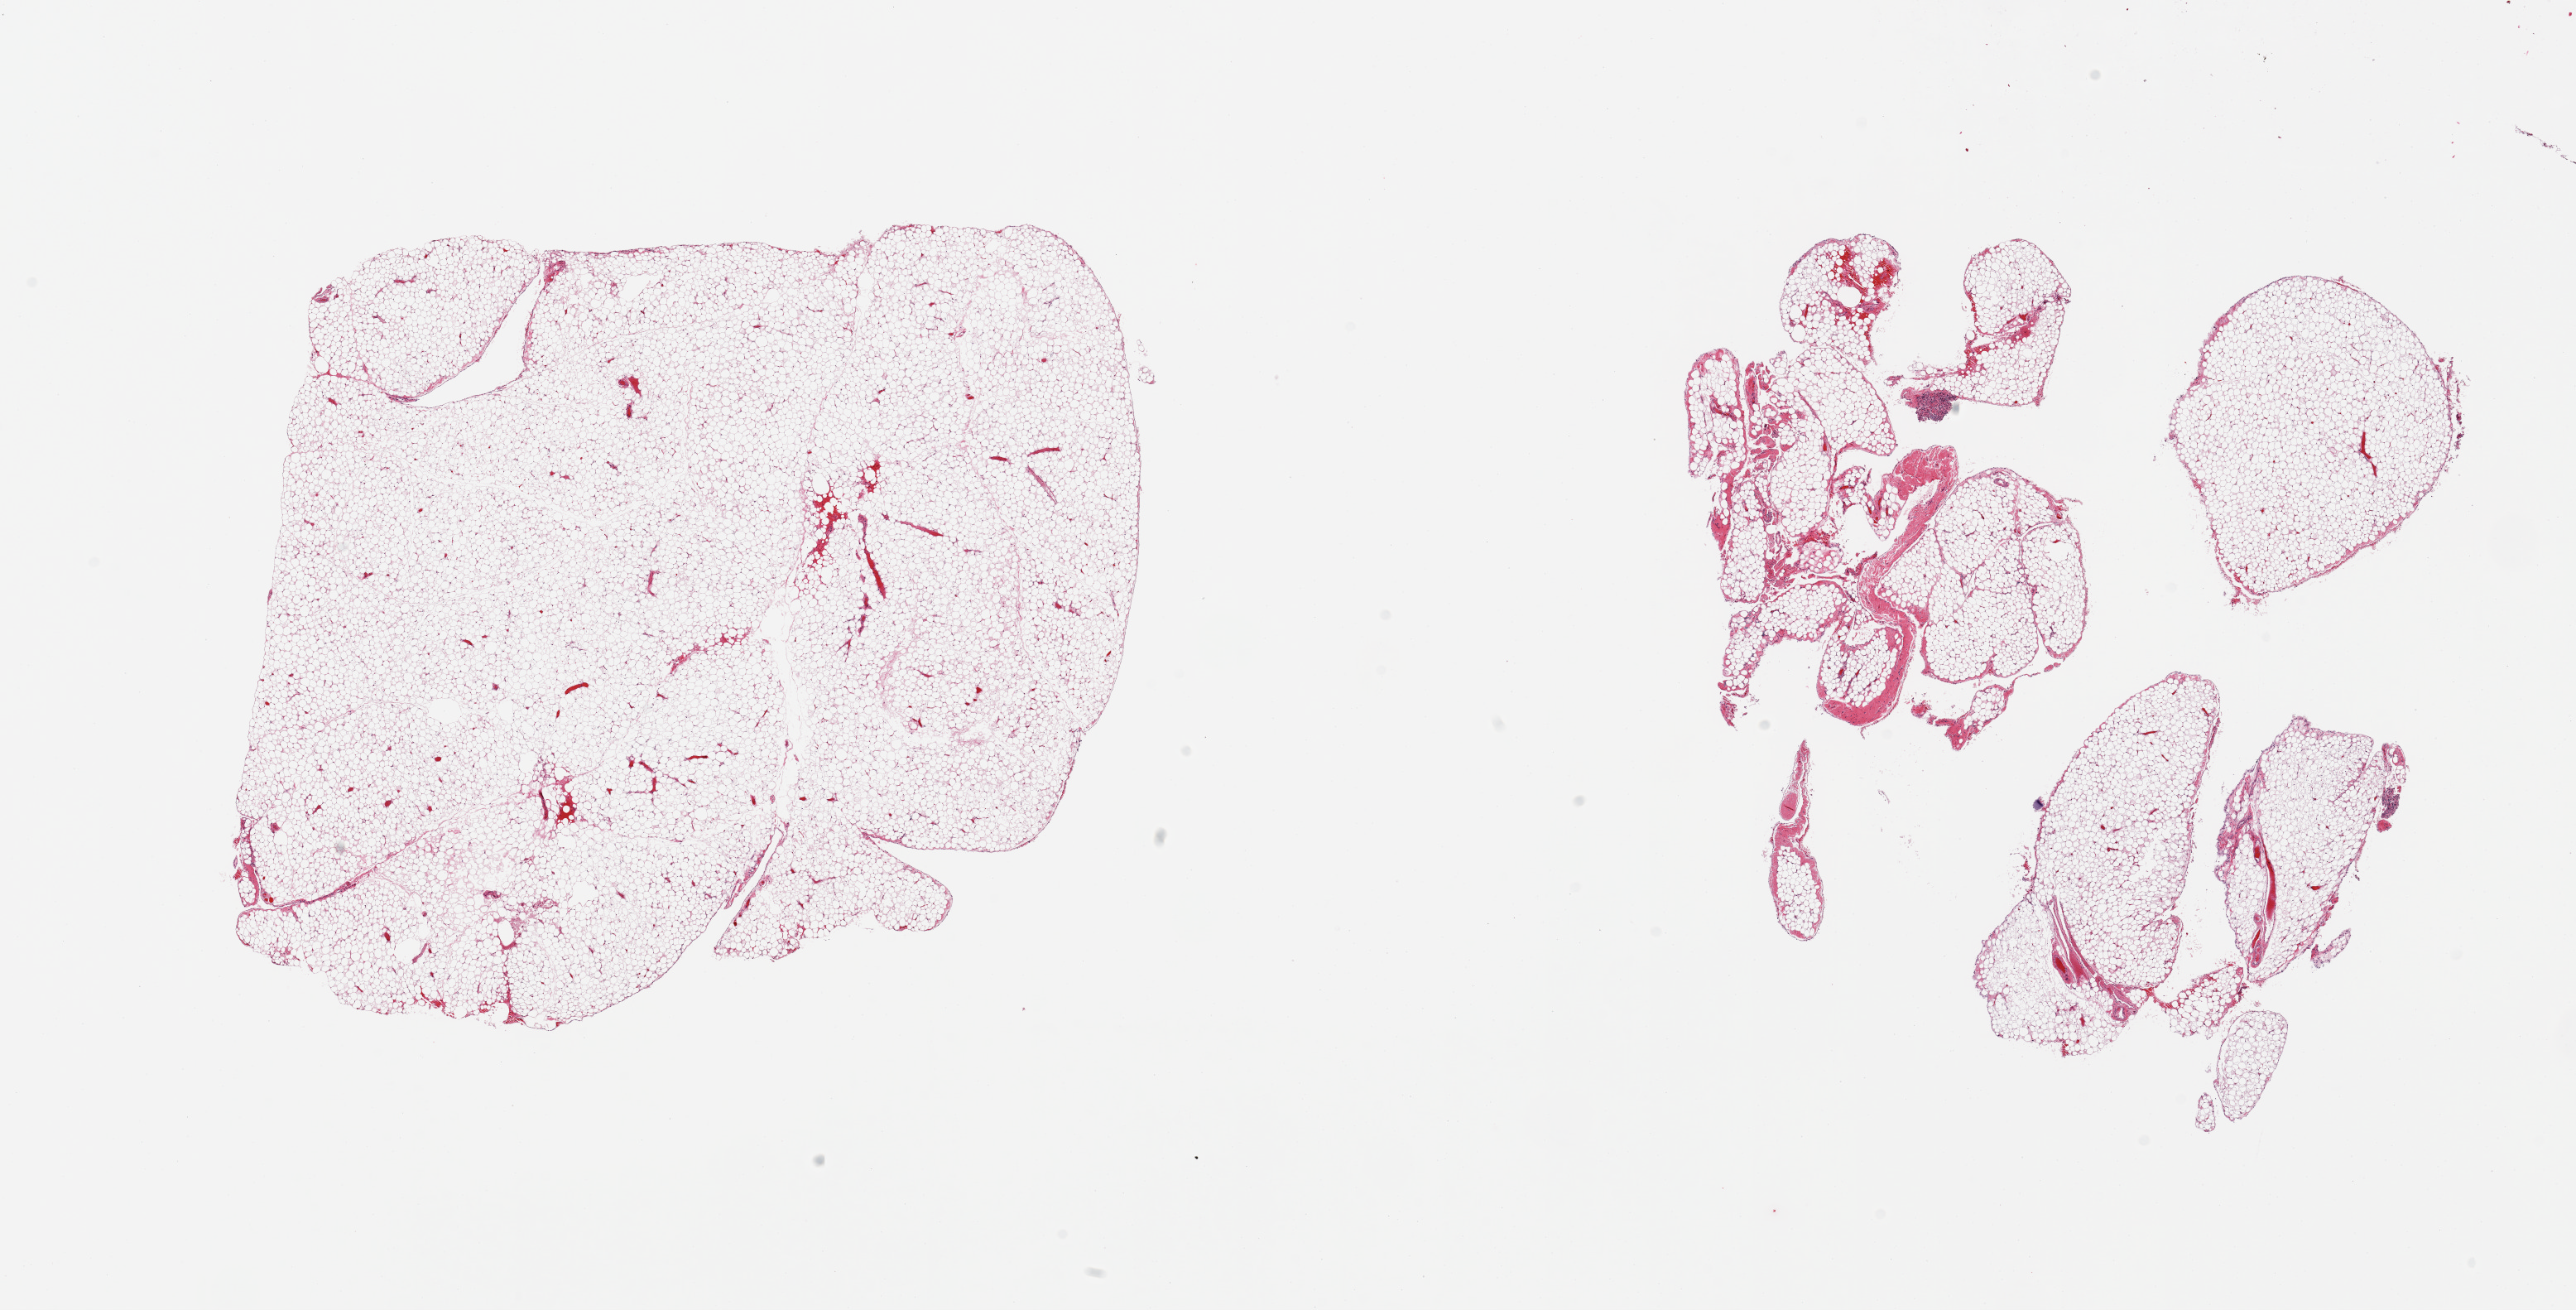
H&E whole-slide image — low-resolution overview of the scanned area, about 24.6 x 12.5 mm (acquisition: 20x scan); PAXgene-fixed, paraffin-embedded tissue; target tissue: omentum; donor tissue sample. Donor: male.
* review note (as recorded): 2 pieces